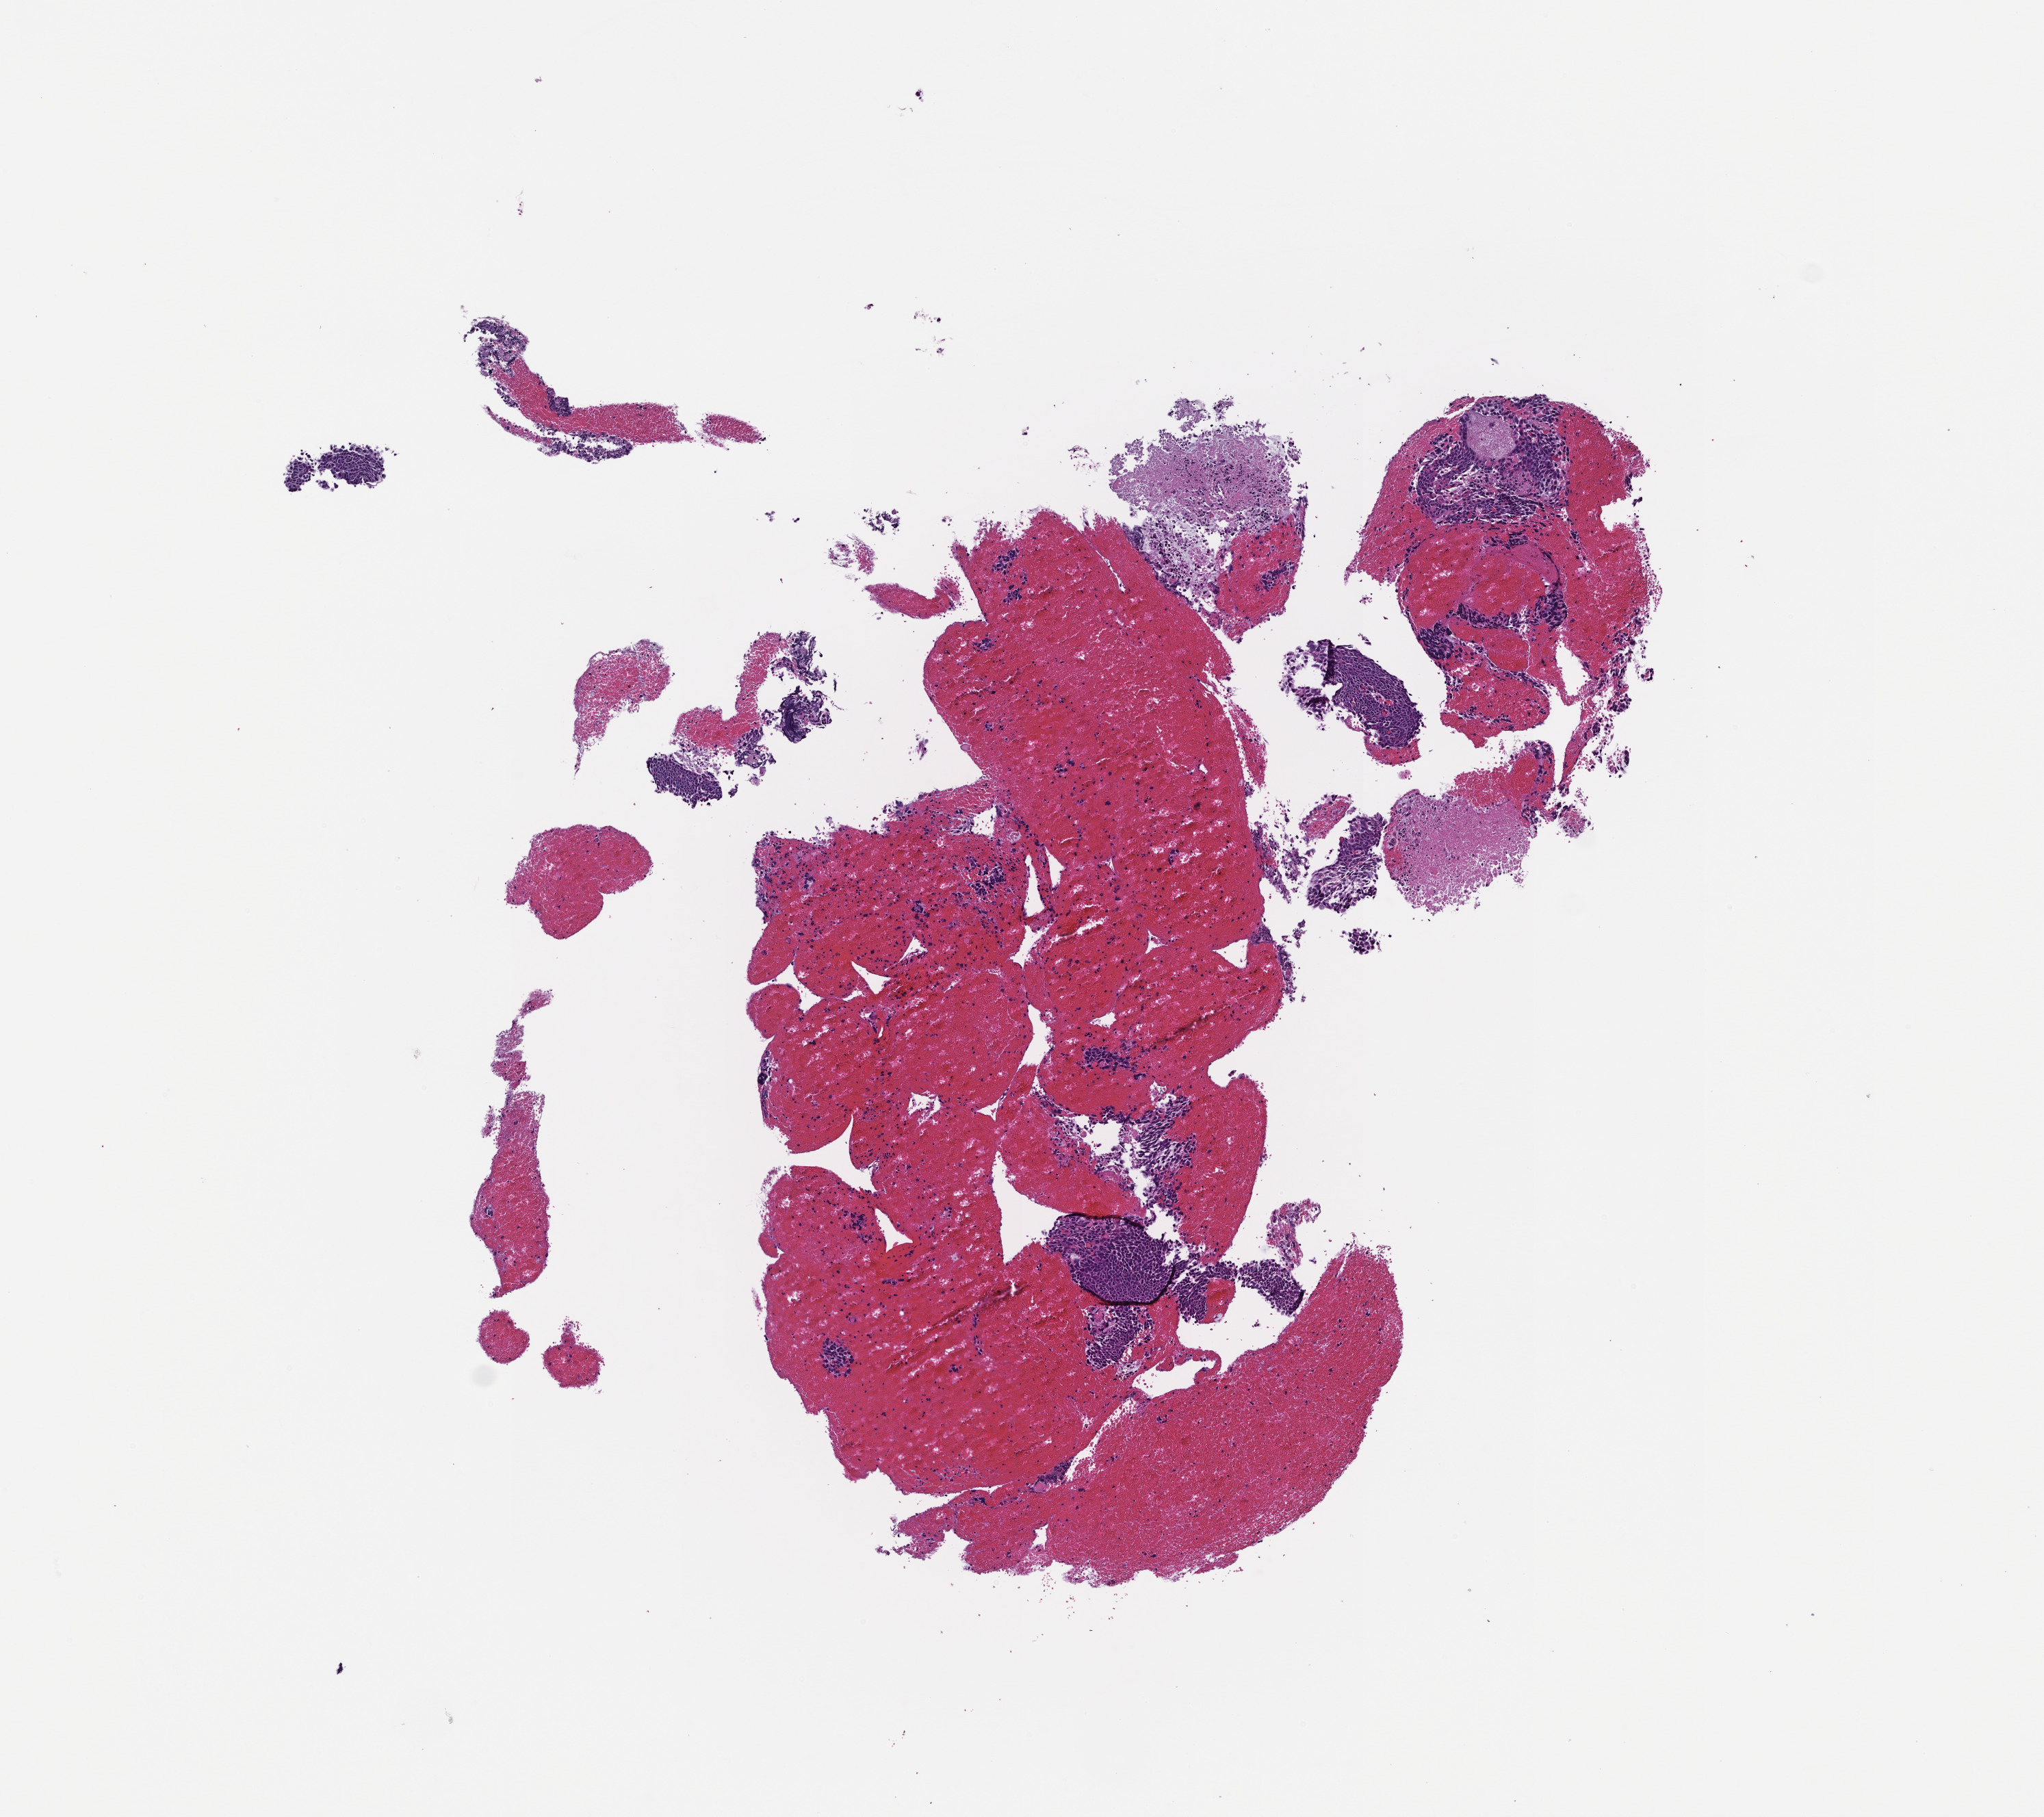
Digitized H&E-stained section — whole scanned area (about 6.0 x 5.4 mm) shown as a low-resolution overview; formalin-fixed, paraffin-embedded (FFPE) tissue. Patient: male.
This section: metastasis (sampled organ not recorded). Primary diagnosis of the patient: Prostate Carcinoma.